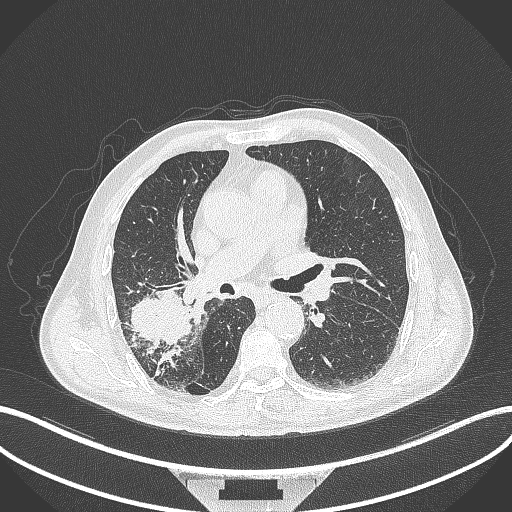
Chest CT, one axial slice. Position 233 of 429 along the scan axis. Reconstruction kernel B70f. 120 kVp. Lung window (W 1500 / L -600 HU). 1 mm slice thickness. 512 × 512 image matrix. Male patient, age 72 years. From the clinical record (not read from this slice): clinical TNM (as recorded): T3 N2 M0.
Outlined on this slice (bounding box drawn by a radiologist):
- lung tumour (recorded histology: adenocarcinoma): bounding box <128,287,202,346> (left, top, right, bottom; pixels)